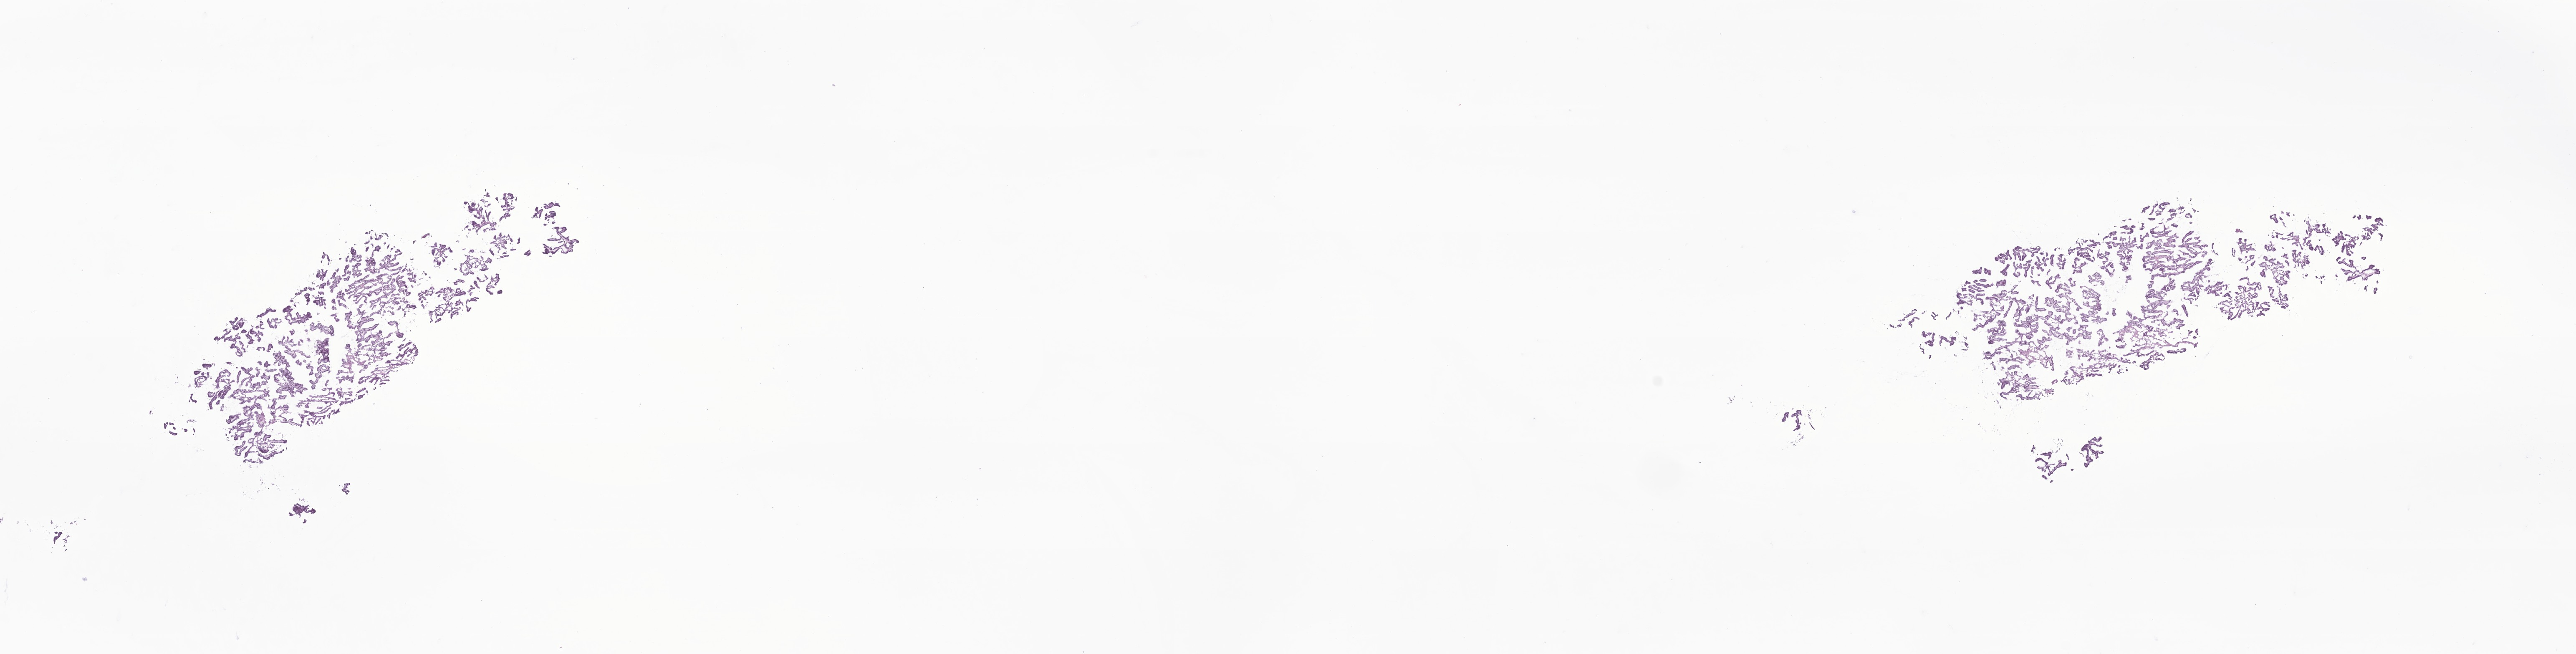
Whole-slide image, H&E stain of tumor tissue from the cerebral ventricle, low-resolution overview of the scanned area, about 26.0 x 6.6 mm; frozen section (OCT-embedded). Patient female; age 764 days (about 2.1 years).
Diagnosis (ICD-O-3 morphology term): Atypical choroid plexus papilloma.